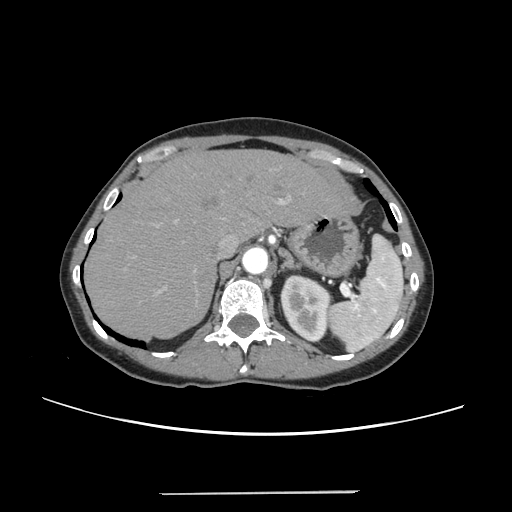
Contrast-enhanced abdominal CT, one axial slice. Slice 181 of 240 in the series (ordered by position). Intravenous contrast given. Soft-tissue window (W 400 / L 40 HU). 1.25 mm slice thickness. 512 × 512 image matrix, field of view 371 × 371 mm. Female patient, age 60 years. From the clinical record (not read from this slice): diagnosis: colorectal cancer liver metastases, imaged before liver resection; multiple liver metastases: no; largest metastasis: 1.5 cm; disease in both lobes: no.
Structures marked on this image (expert manual segmentation):
- liver: box from (x=87, y=150) to (x=347, y=338) px
- planned liver remnant (the part of the liver to remain after resection): (x=87, y=150)–(x=345, y=338)
- portal vein (with intrahepatic branches): (x=134, y=197)–(x=291, y=294)